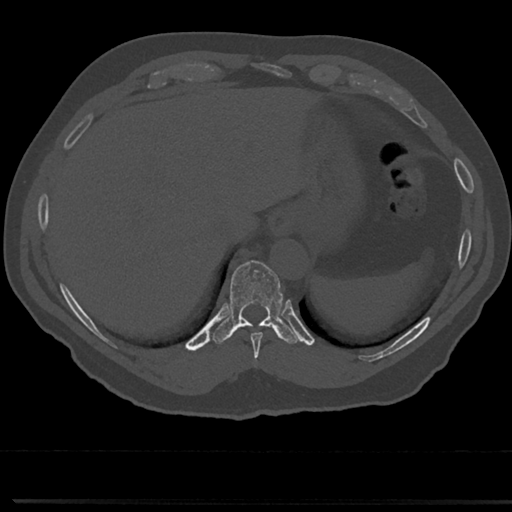
CT including the spine, one axial slice. Slice 270 of 817 in the series (ordered by position). Reconstruction kernel Br40s/3. 120 kVp. Bone window (W 1800 / L 400 HU). 0.5 mm slice thickness. 512 × 512 image matrix, field of view 355 × 355 mm. Male patient, age 61 years. Case-level facts recorded for this patient, not image findings: primary cancer: prostate.
Annotated regions visible in this slice (semi-automatic segmentation, software-assisted and operator-edited):
- T10 vertebra: bounding box [x1, y1, x2, y2] px = [229, 261, 282, 324]
- T9 vertebra: [237, 322, 279, 353]